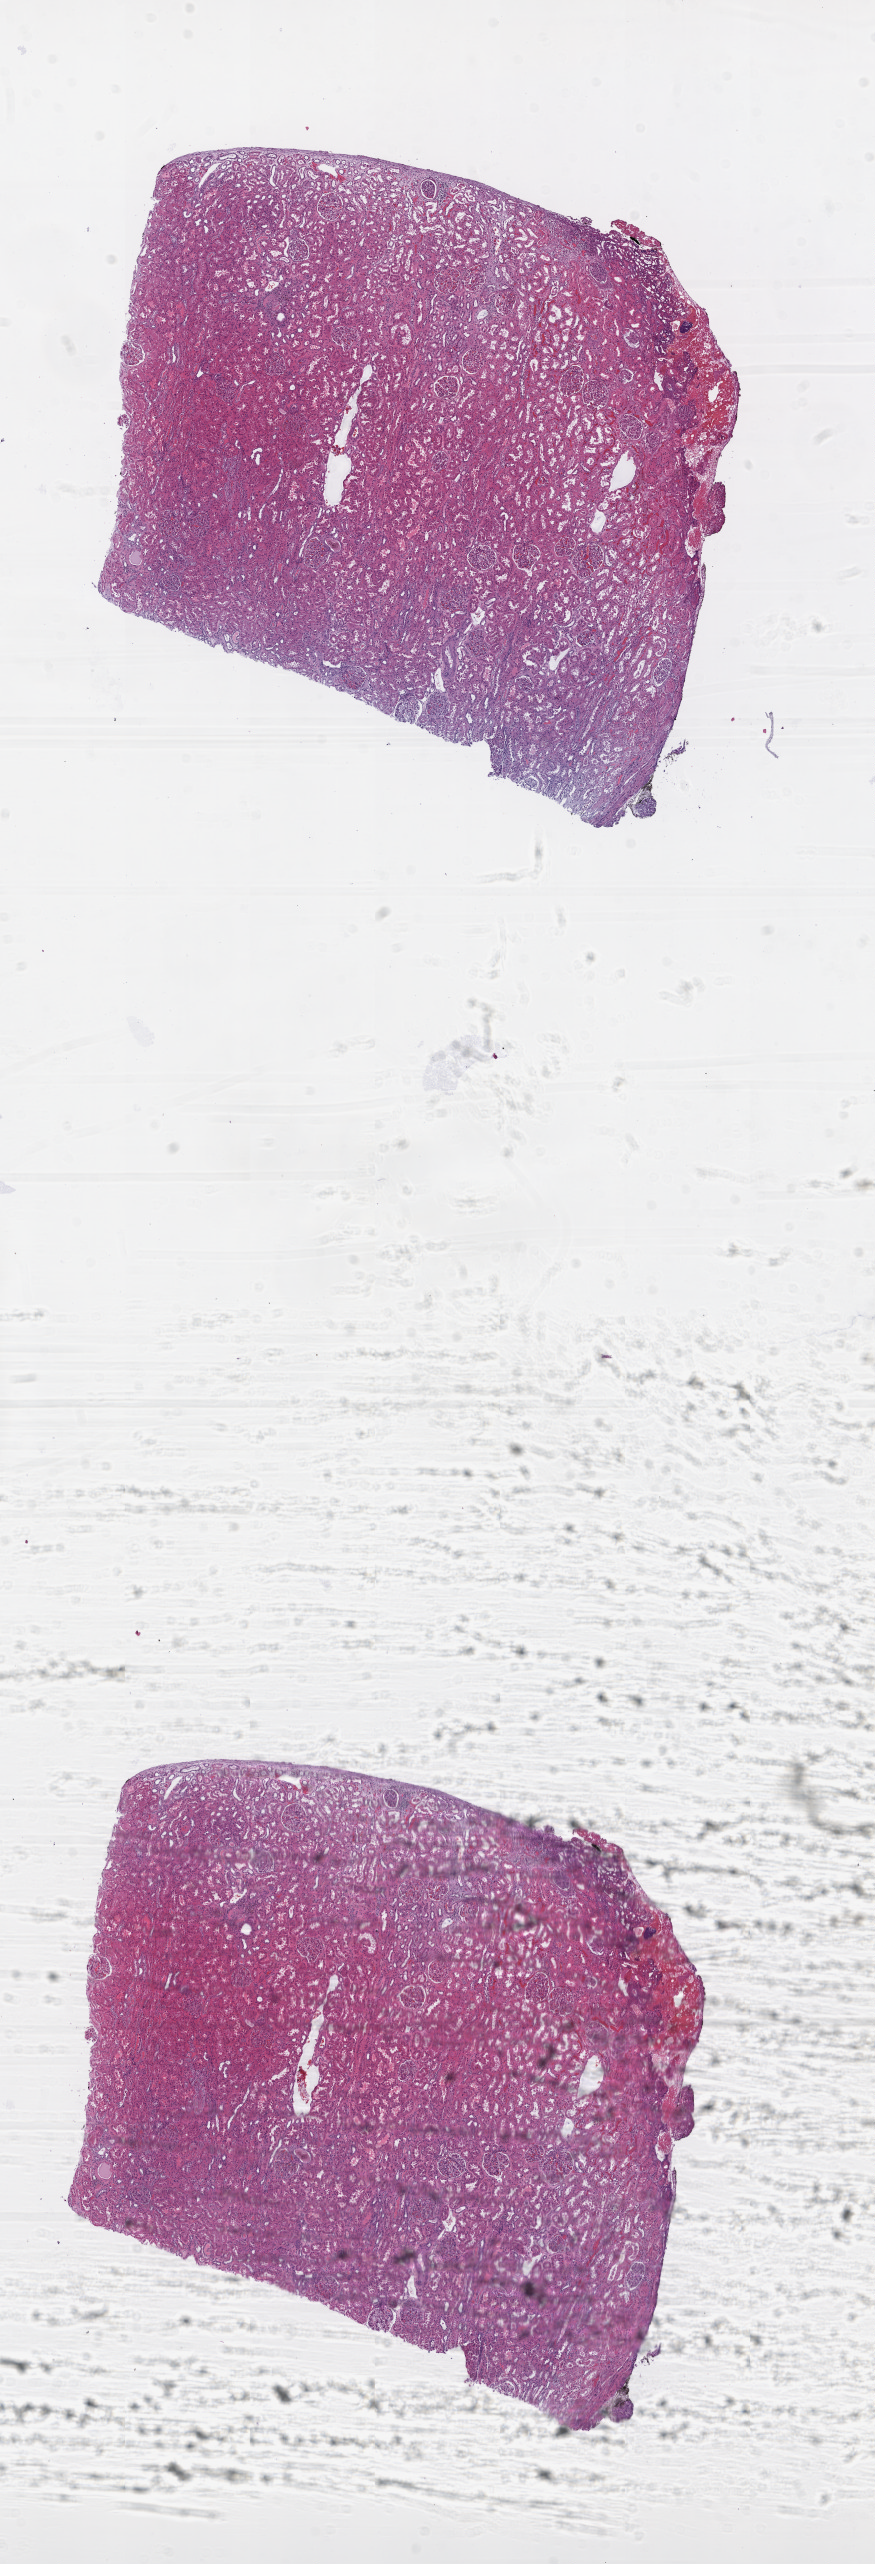
Digitized H&E-stained tissue section (whole slide), whole scanned area (about 7.0 x 20.6 mm) shown as a low-resolution overview, frozen section from the top of the tissue portion, kidney, solid tissue normal (non-tumour tissue) sample. Male, age 52 years at initial diagnosis.
- this section: solid tissue normal sample (biorepository sample class)
- patient diagnosis: Papillary adenocarcinoma, NOS